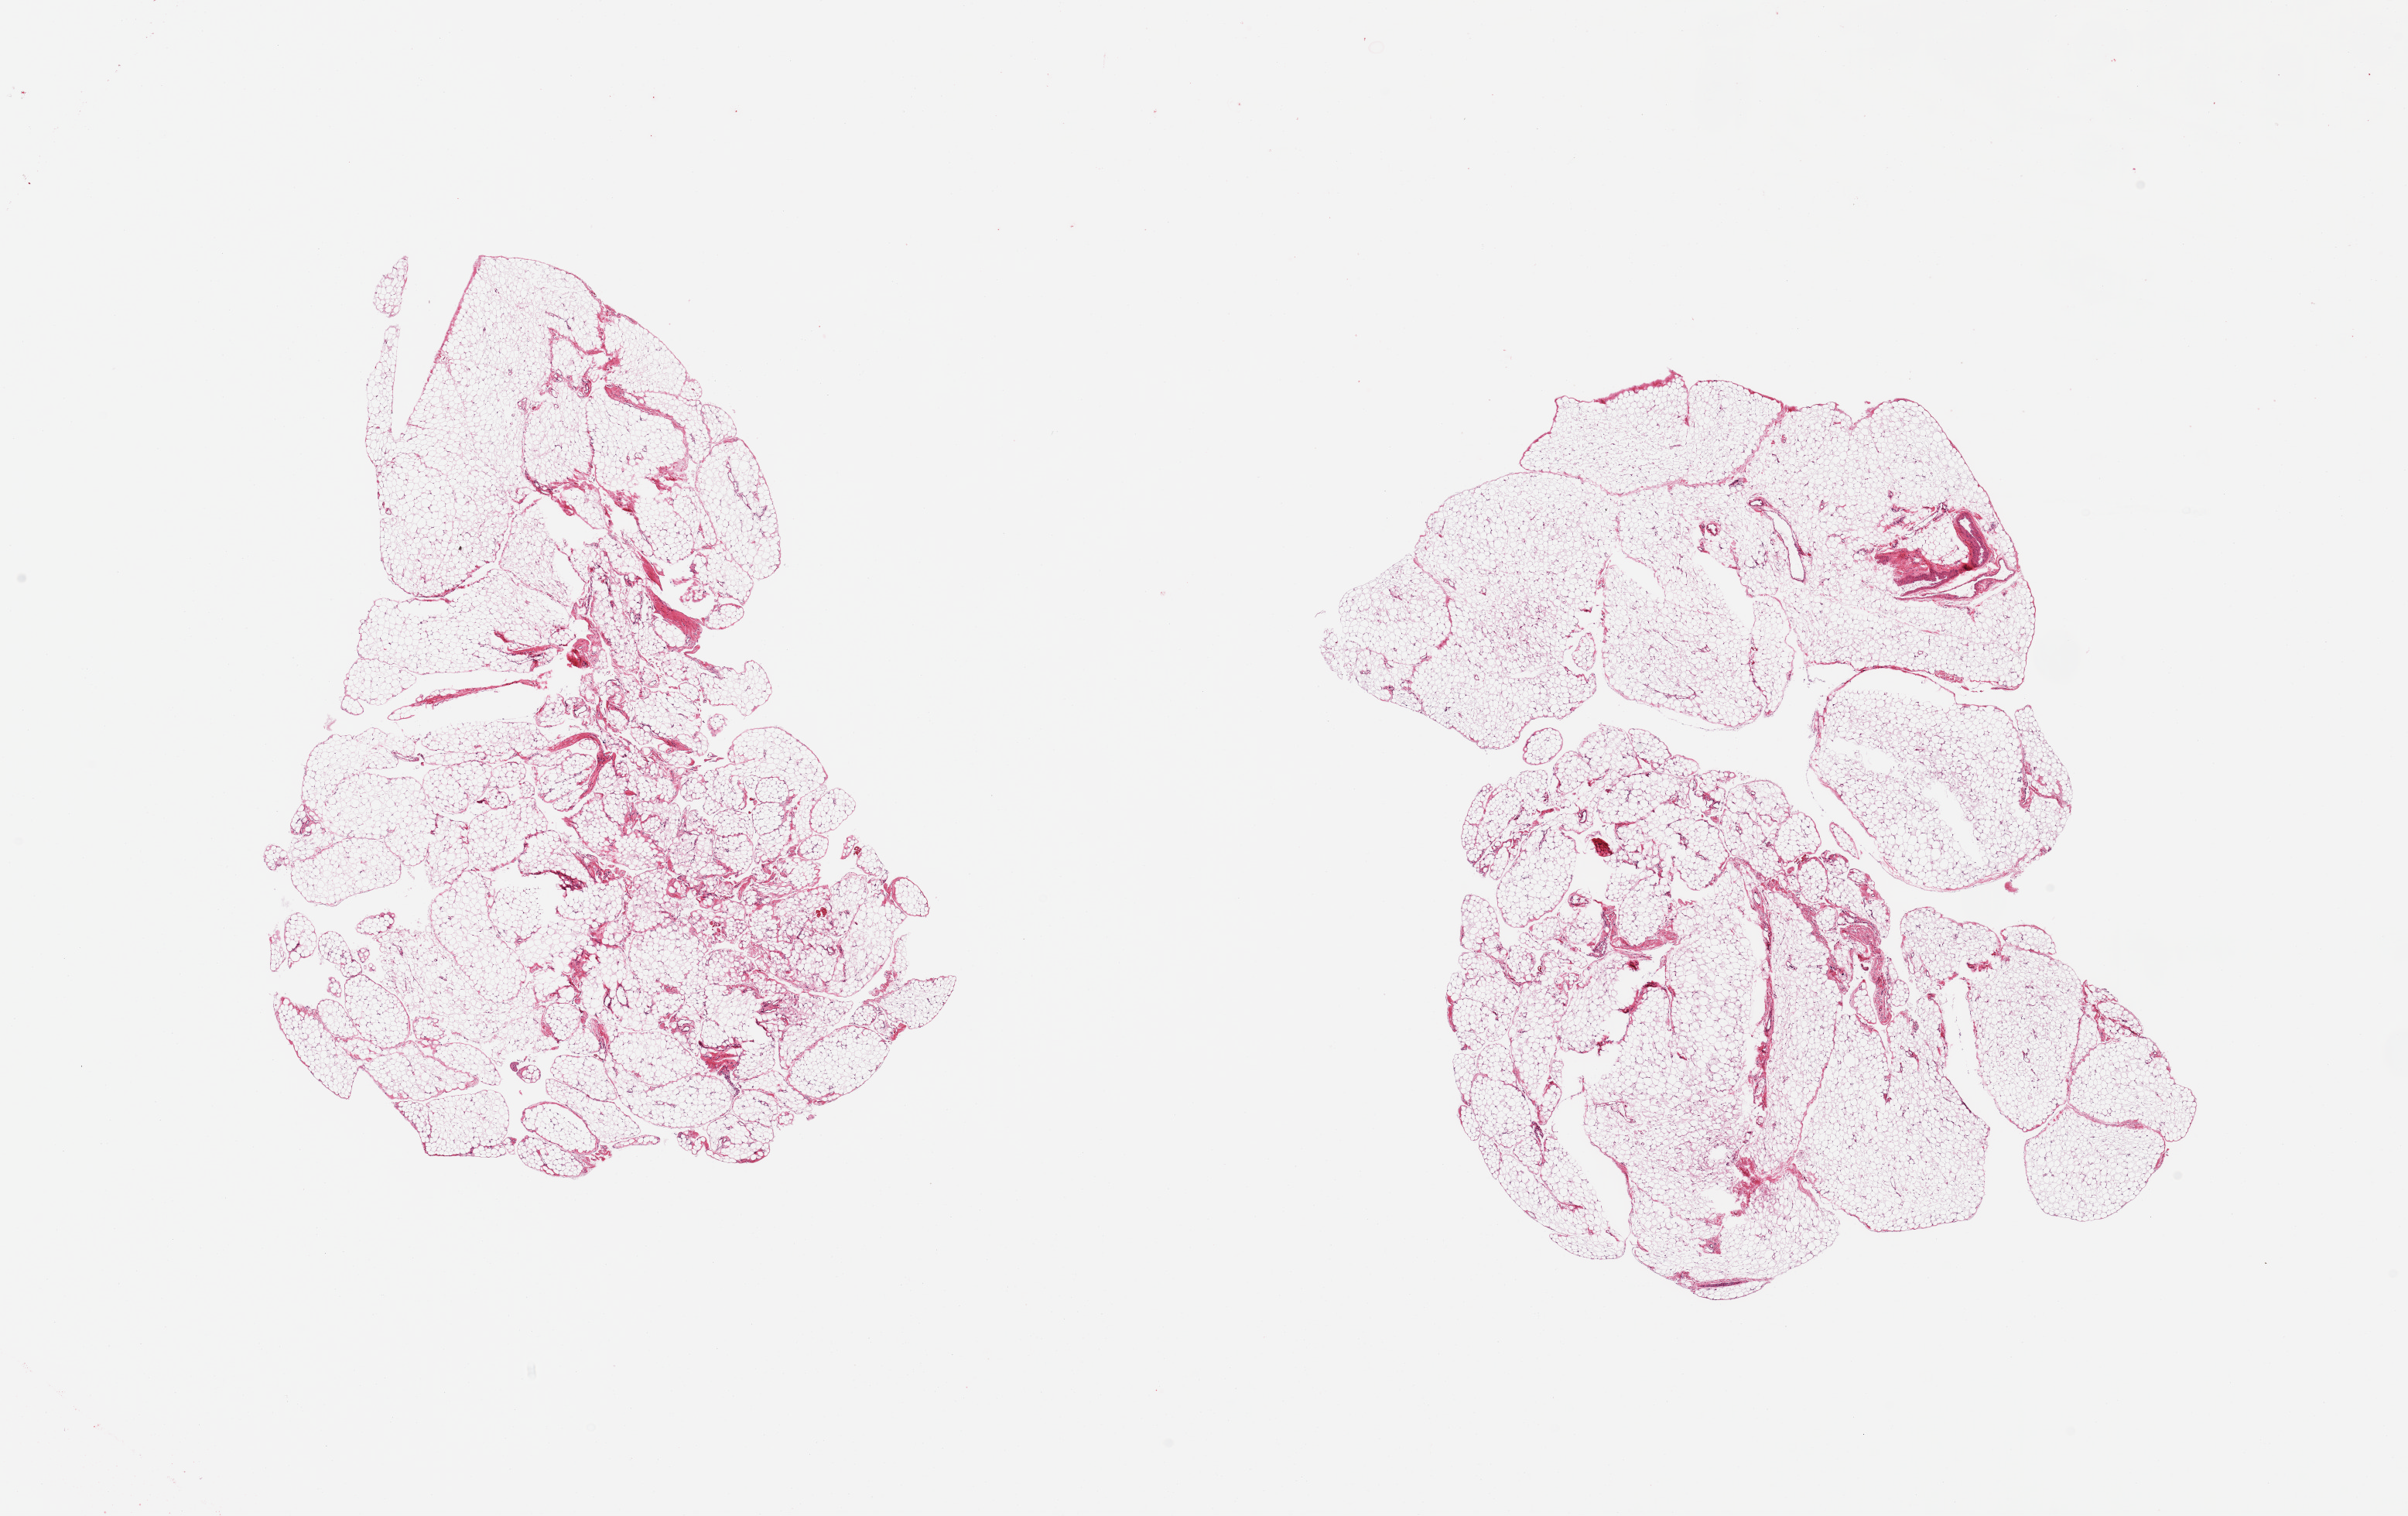
H&E whole-slide image, brightfield, whole scanned area (about 24.6 x 15.5 mm) shown as a low-resolution overview; PAXgene-fixed paraffin-embedded (PFPE) section; sampled site (target tissue): omentum; tissue donor sample.
Review note (as recorded): 2 pieces, ~5% fascia/vascular elements.